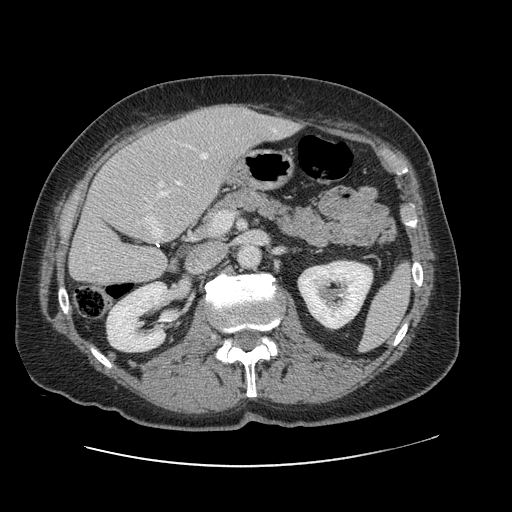
Contrast-enhanced abdominal CT, one axial slice; position 46 of 138 along the scan axis; 120 kVp; intravenous contrast given; soft-tissue window (W 400 / L 40 HU); 2.5 mm slice thickness; 512 × 512 image matrix. Male patient, age 71 years. Case-level facts recorded for this patient, not image findings: diagnosis: colorectal cancer liver metastases, imaged before liver resection; multiple liver metastases: no.
Structures marked on this image (manually delineated by an expert):
- hepatic veins: bounding box <94,130,276,269> (left, top, right, bottom; pixels)
- liver: <70,105,297,286>
- planned liver remnant (the part of the liver to remain after resection): <70,138,196,286>
- portal vein (with intrahepatic branches): <159,182,163,187>